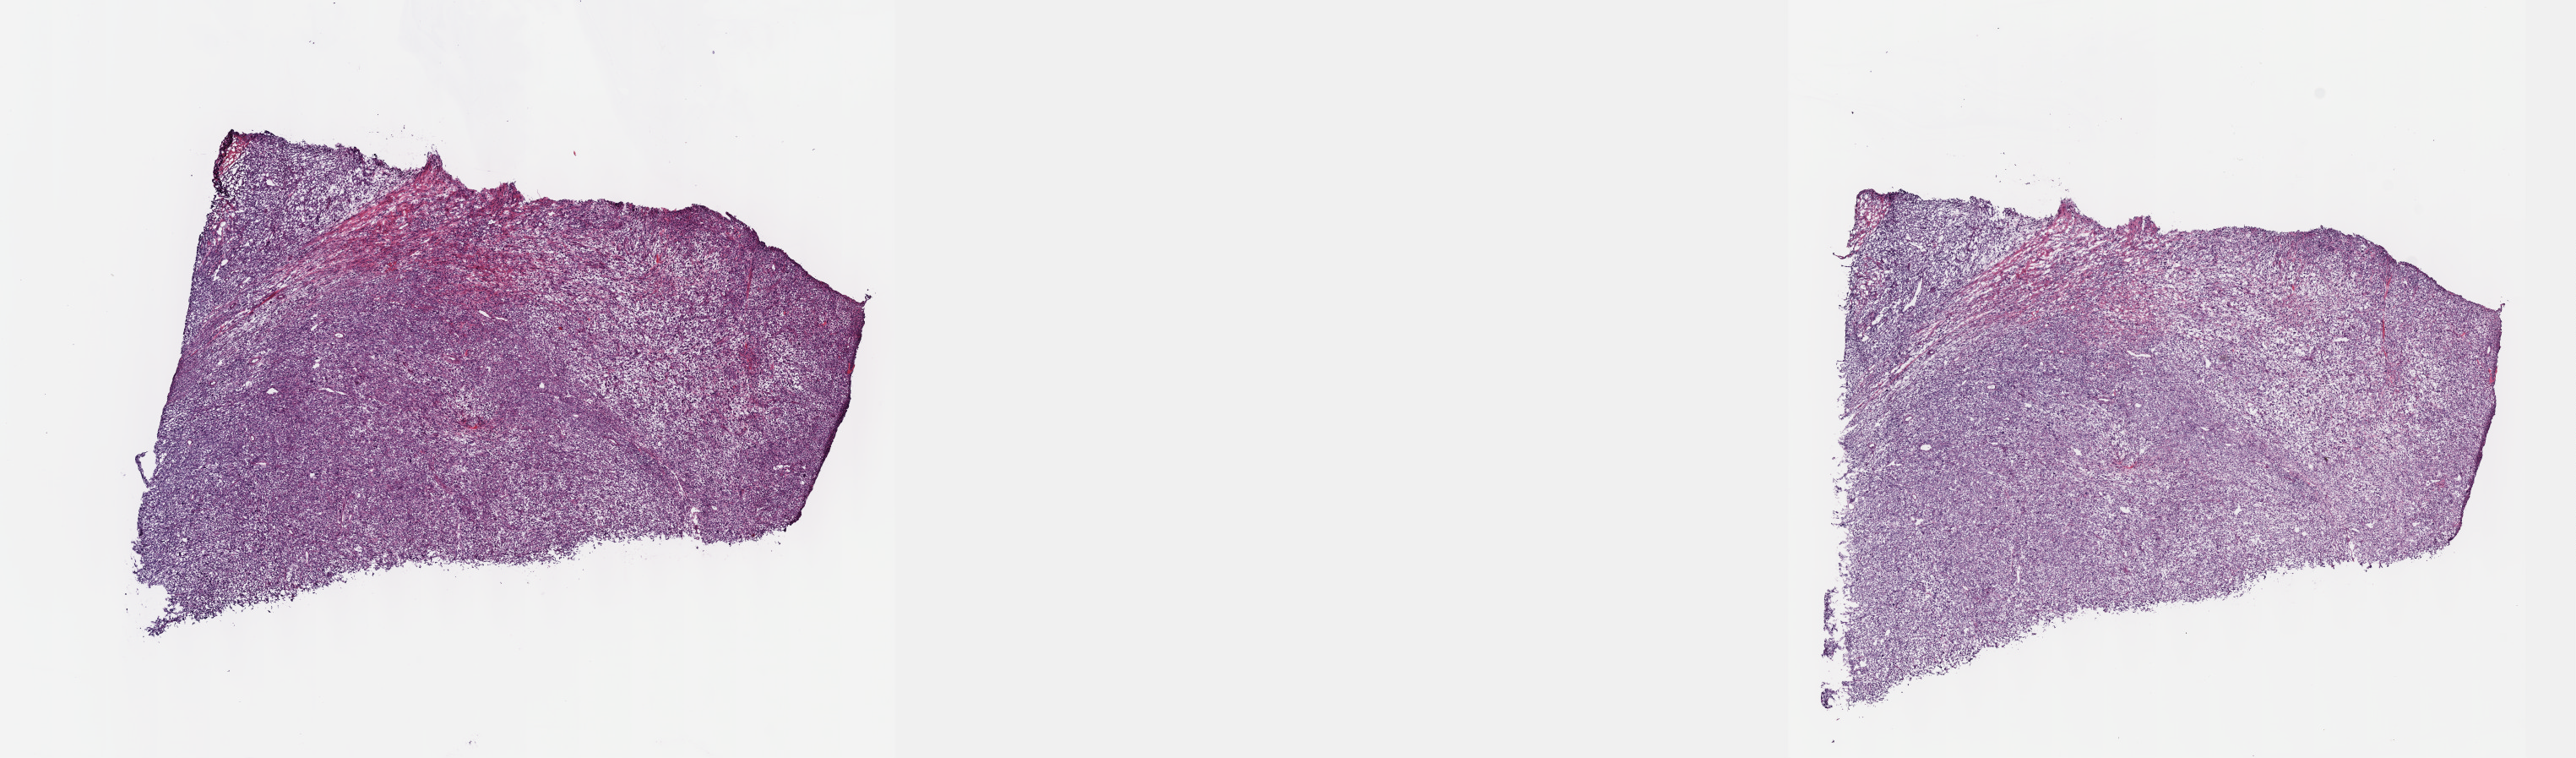
Digitized H&E tissue section (whole slide) — a low-resolution overview of the entire scanned area, about 24.6 x 7.2 mm; frozen section from the top of the tissue portion; connective, subcutaneous and other soft tissues, primary tumour sample. Male patient; age at initial diagnosis 78 years. Slide review estimates, as recorded: tumour cells 90%, tumour nuclei 80%, normal cells 0%, stromal cells 10%, necrosis 0%. Inflammatory infiltration, as recorded: lymphocyte infiltration 0%, monocyte infiltration 0%, neutrophil infiltration 0%.
- histologic diagnosis: Undifferentiated sarcoma (connective, subcutaneous and other soft tissues of upper limb and shoulder)